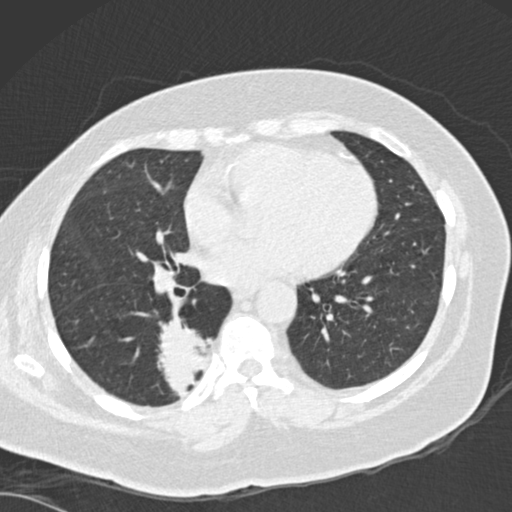
Low-dose screening chest CT, one axial slice. Slice 69 of 162 in the series (ordered by position). Reconstruction kernel B30f. Lung window (W 1500 / L -600 HU). 512 × 512 image matrix.
Structures marked on this image (outlined manually by an expert reader):
- lesion 1 (tumor, lower lobe of right lung): bounding box [x1, y1, x2, y2] px = [157, 313, 212, 398]